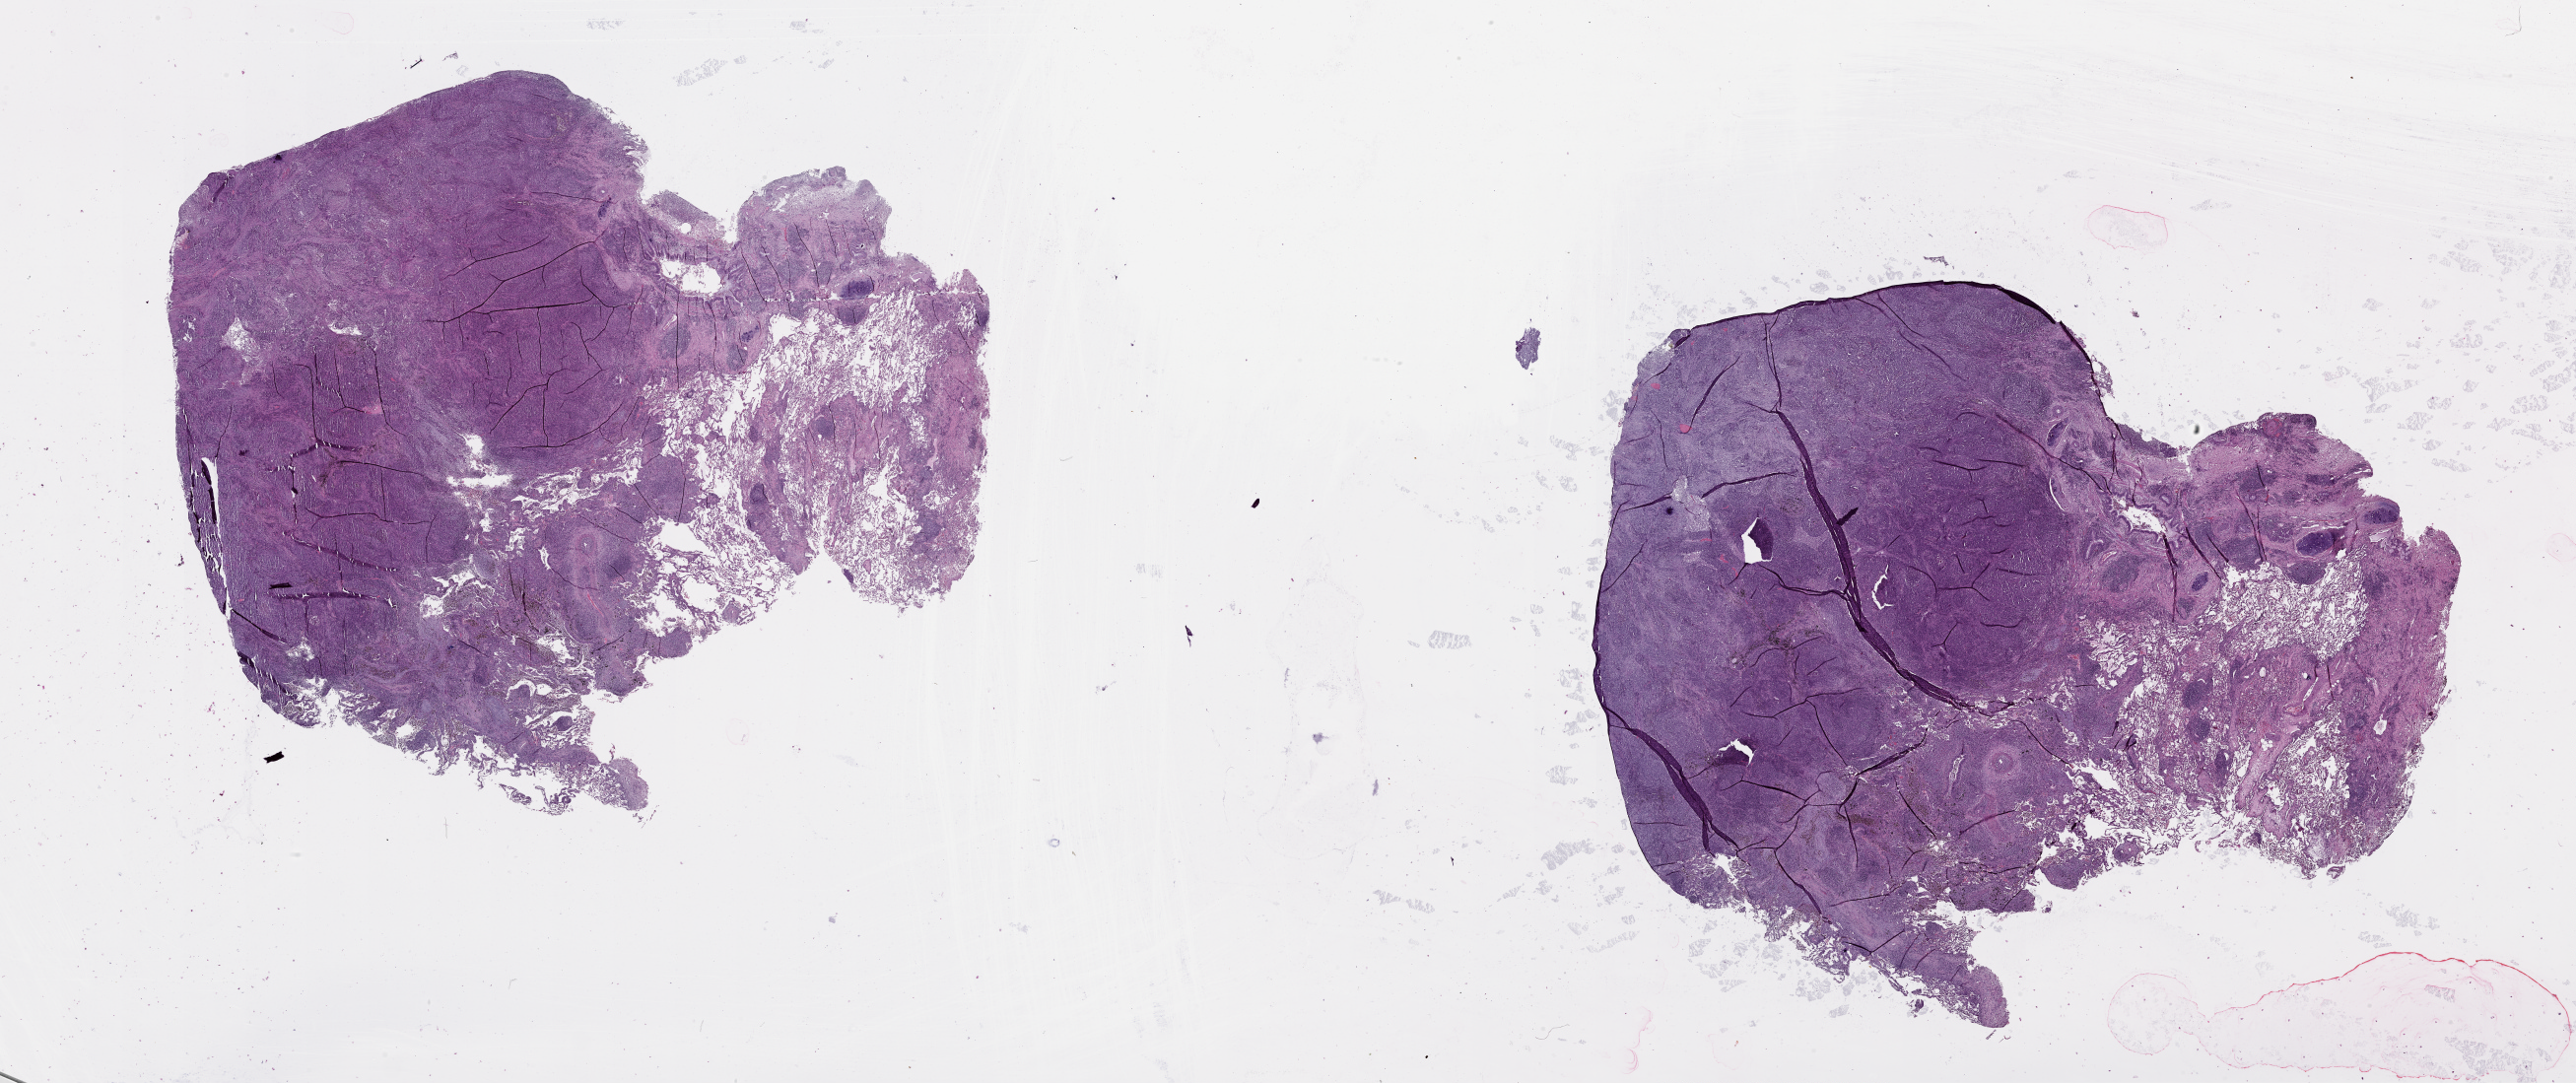
Whole-slide histology image, Hematoxylin and eosin (H&E) stained, low-resolution overview of the scanned area, about 42.1 x 17.7 mm (slide scanned at 20x); lung, tumour tissue. Male, 65 y/o.
Patient diagnosis (cohort enrolment): squamous cell carcinoma (lung).